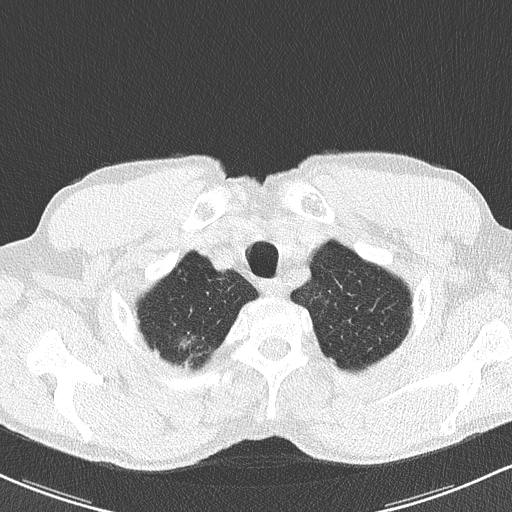
Low-dose screening chest CT, axial slice. Baseline screening round. Lung window (W 1500 / L -600 HU). 2 mm slice thickness. Lung (sharp) reconstruction kernel (B50f). Male participant, aged 62 years at enrolment. Former smoker at enrolment.
Expert-annotated lung lesion, bounding box [x1, y1, x2, y2] px = [163, 327, 208, 366]. The exam's reader record, not a measurement of the box and not confirmed to be the same lesion: non-calcified nodule or mass ≥4 mm, right upper lobe, 12 × 9 mm, spiculated (stellate) margins, soft tissue attenuation. Official screen result: positive, change unspecified: nodule(s) >= 4 mm or enlarging nodule(s), mass(es), or other non-specific abnormalities suspicious for lung cancer. Later outcome: lung cancer diagnosed 398 days after this screen — bronchiolo-alveolar adenocarcinoma, NOS, right upper lobe, well differentiated (G1), stage IA (AJCC 6th edition), 15 mm at pathology.